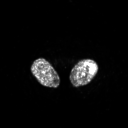
FDG PET of an extremity soft-tissue mass (from a PET/CT study), one axial slice; position 189 of 267 along the scan axis; 3.27 mm slice thickness; 128 × 128 image matrix, field of view 700 × 700 mm. Patient: female, 62 years. From the clinical record (not read from this slice): histological type: undifferentiated – high grade; grade: high; site of the primary tumour: left thigh.
Outlined on this slice (expert contour drawn on MRI and transferred to this co-registered scan by the dataset authors):
- gross tumour volume including surrounding oedema: bounding box <90,67,93,70> (left, top, right, bottom; pixels)